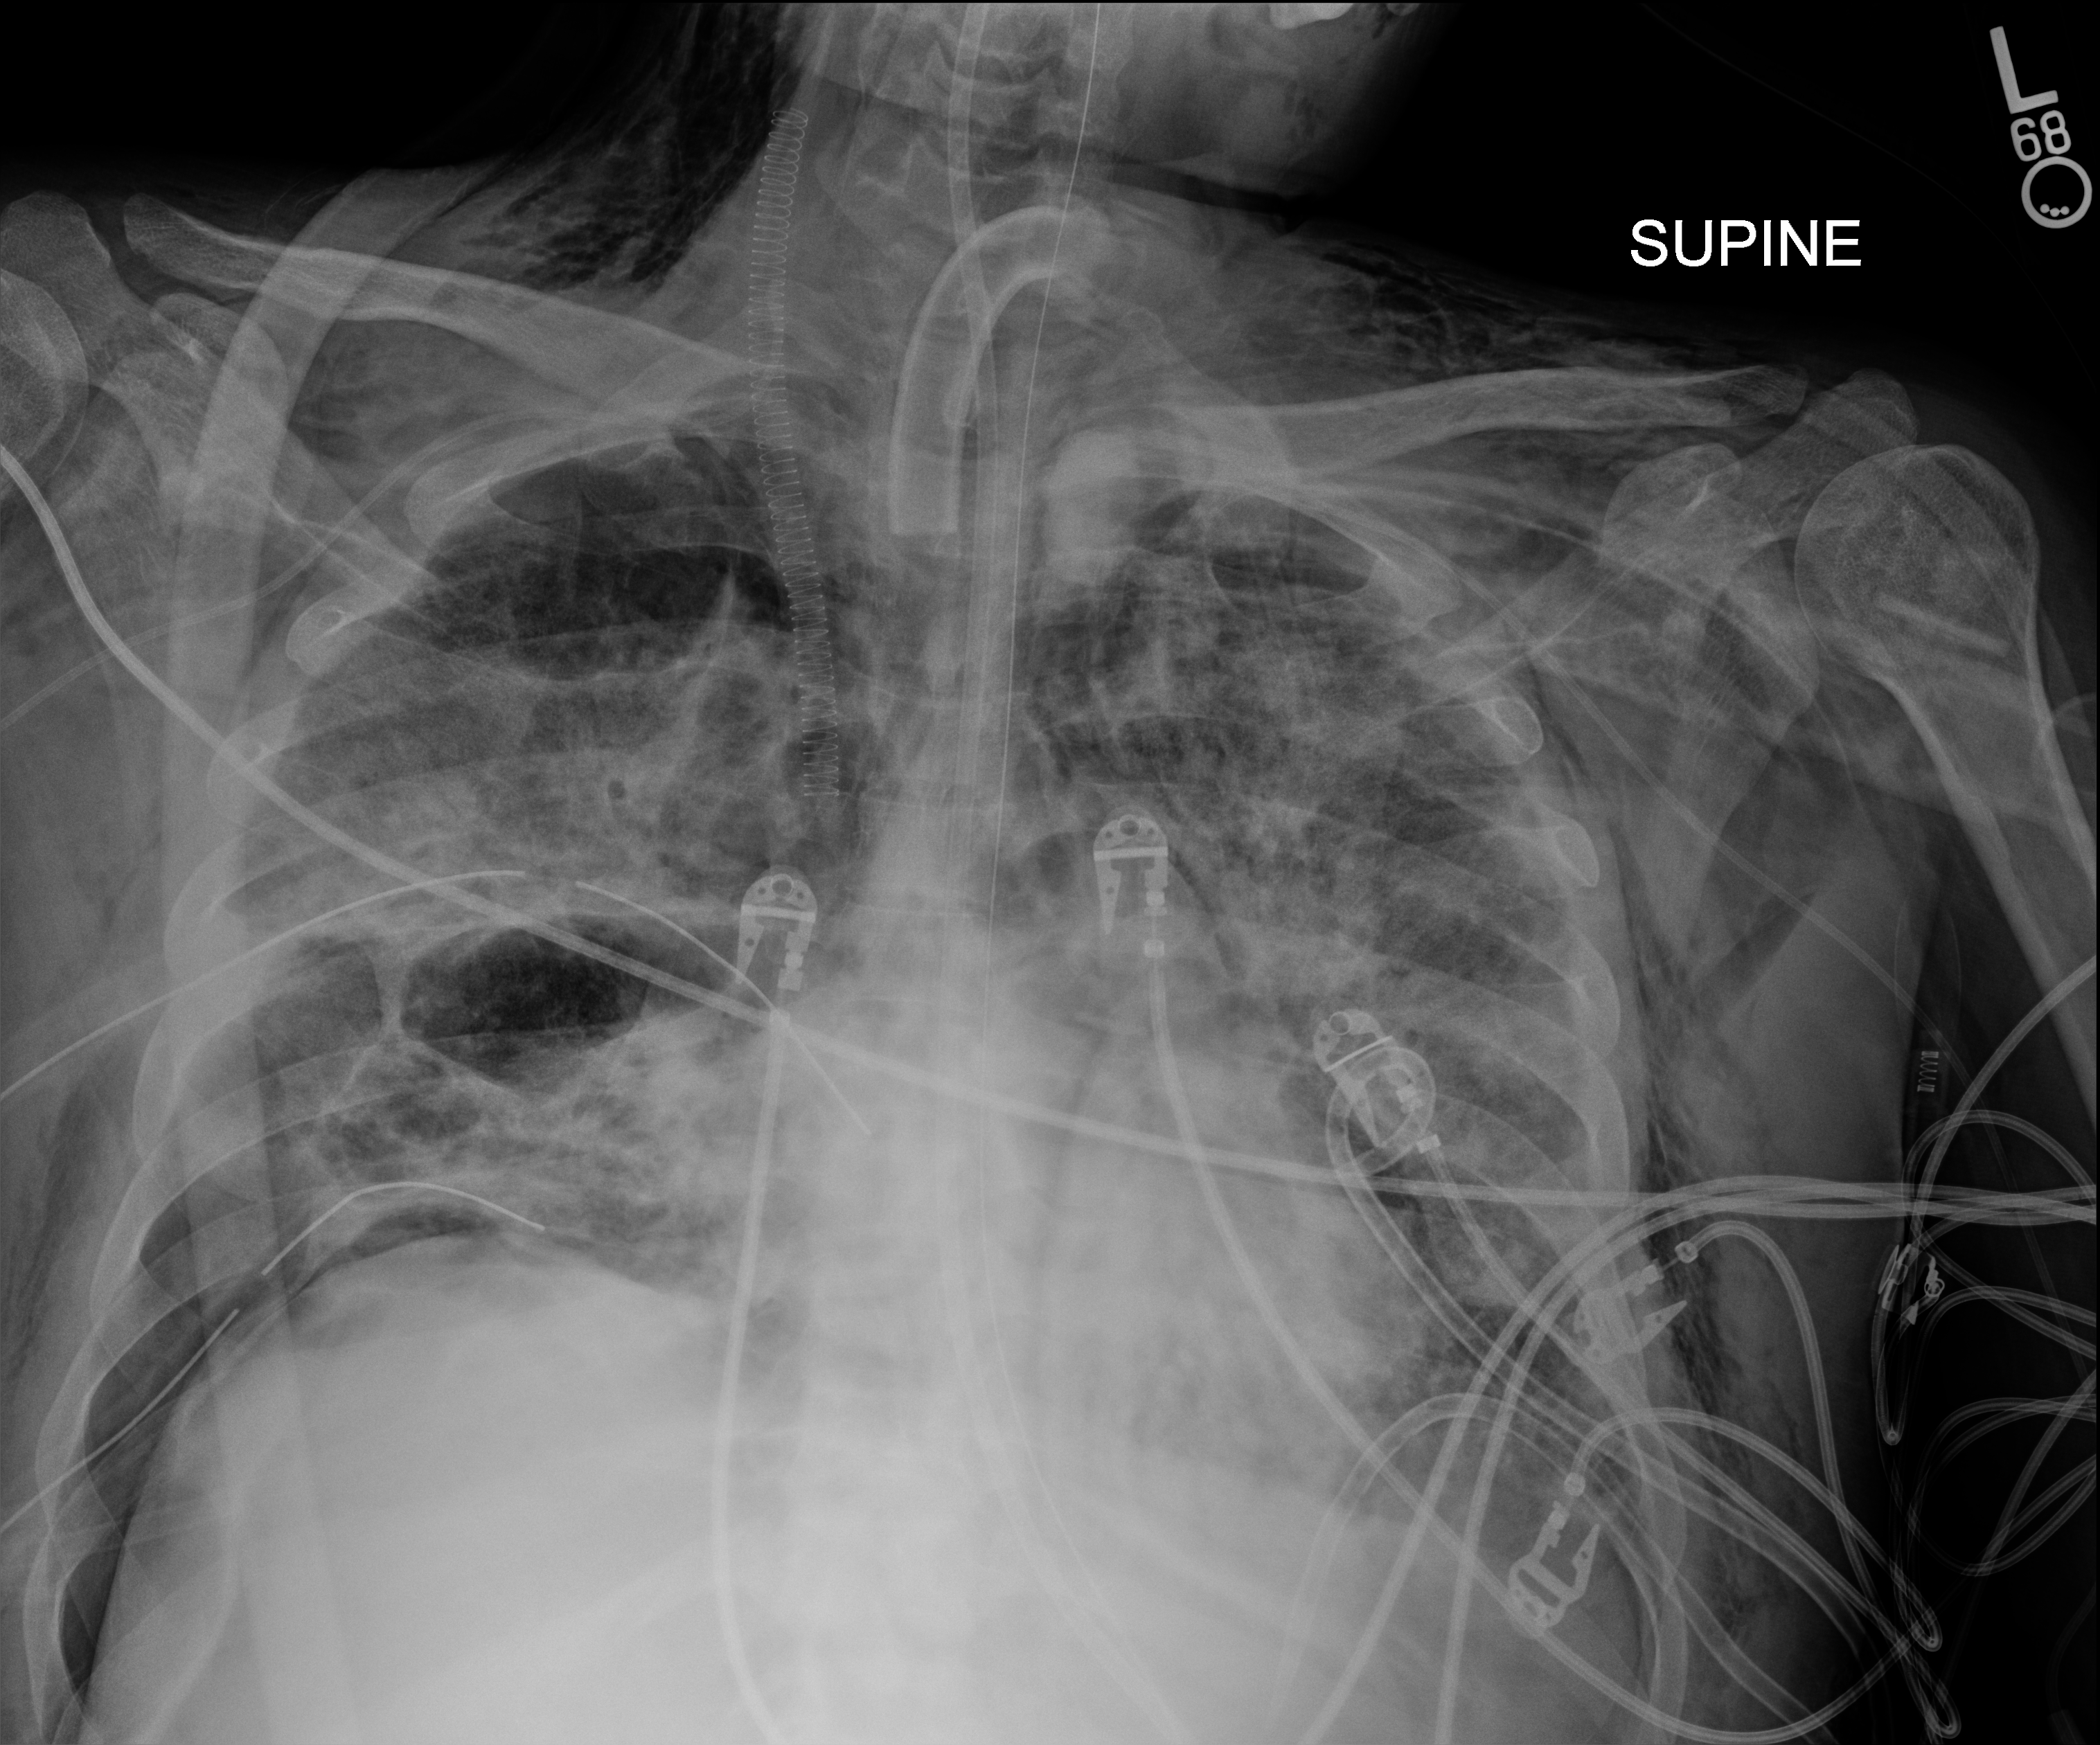
Chest radiograph (digital radiography). Patient hospitalised with COVID-19, aged 18–59 years.
Admission-level facts for this patient (not findings on this image; timing relative to this image not recorded): length of hospital stay: 60 days; mechanically ventilated during this hospital stay: yes; admitted to intensive care during this hospital stay: yes.